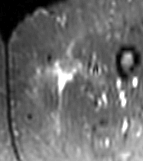
MRI of an extremity soft-tissue mass, one axial slice. Slice 2 of 81 in the series (ordered by position). STIR. MR volume resampled by the dataset authors to the PET/CT grid (not the native acquisition matrix). 143 × 161 image matrix. Female patient. Case-level facts recorded for this patient, not image findings: histological type: myxofibrosarcoma; grade: intermediate; site of the primary tumour: left thigh.
Structures marked on this image (expert contour drawn on MRI and transferred to this co-registered scan by the dataset authors):
- gross tumour volume including surrounding oedema: bounding box (x1, y1, x2, y2) in pixels: (51, 63, 105, 88)